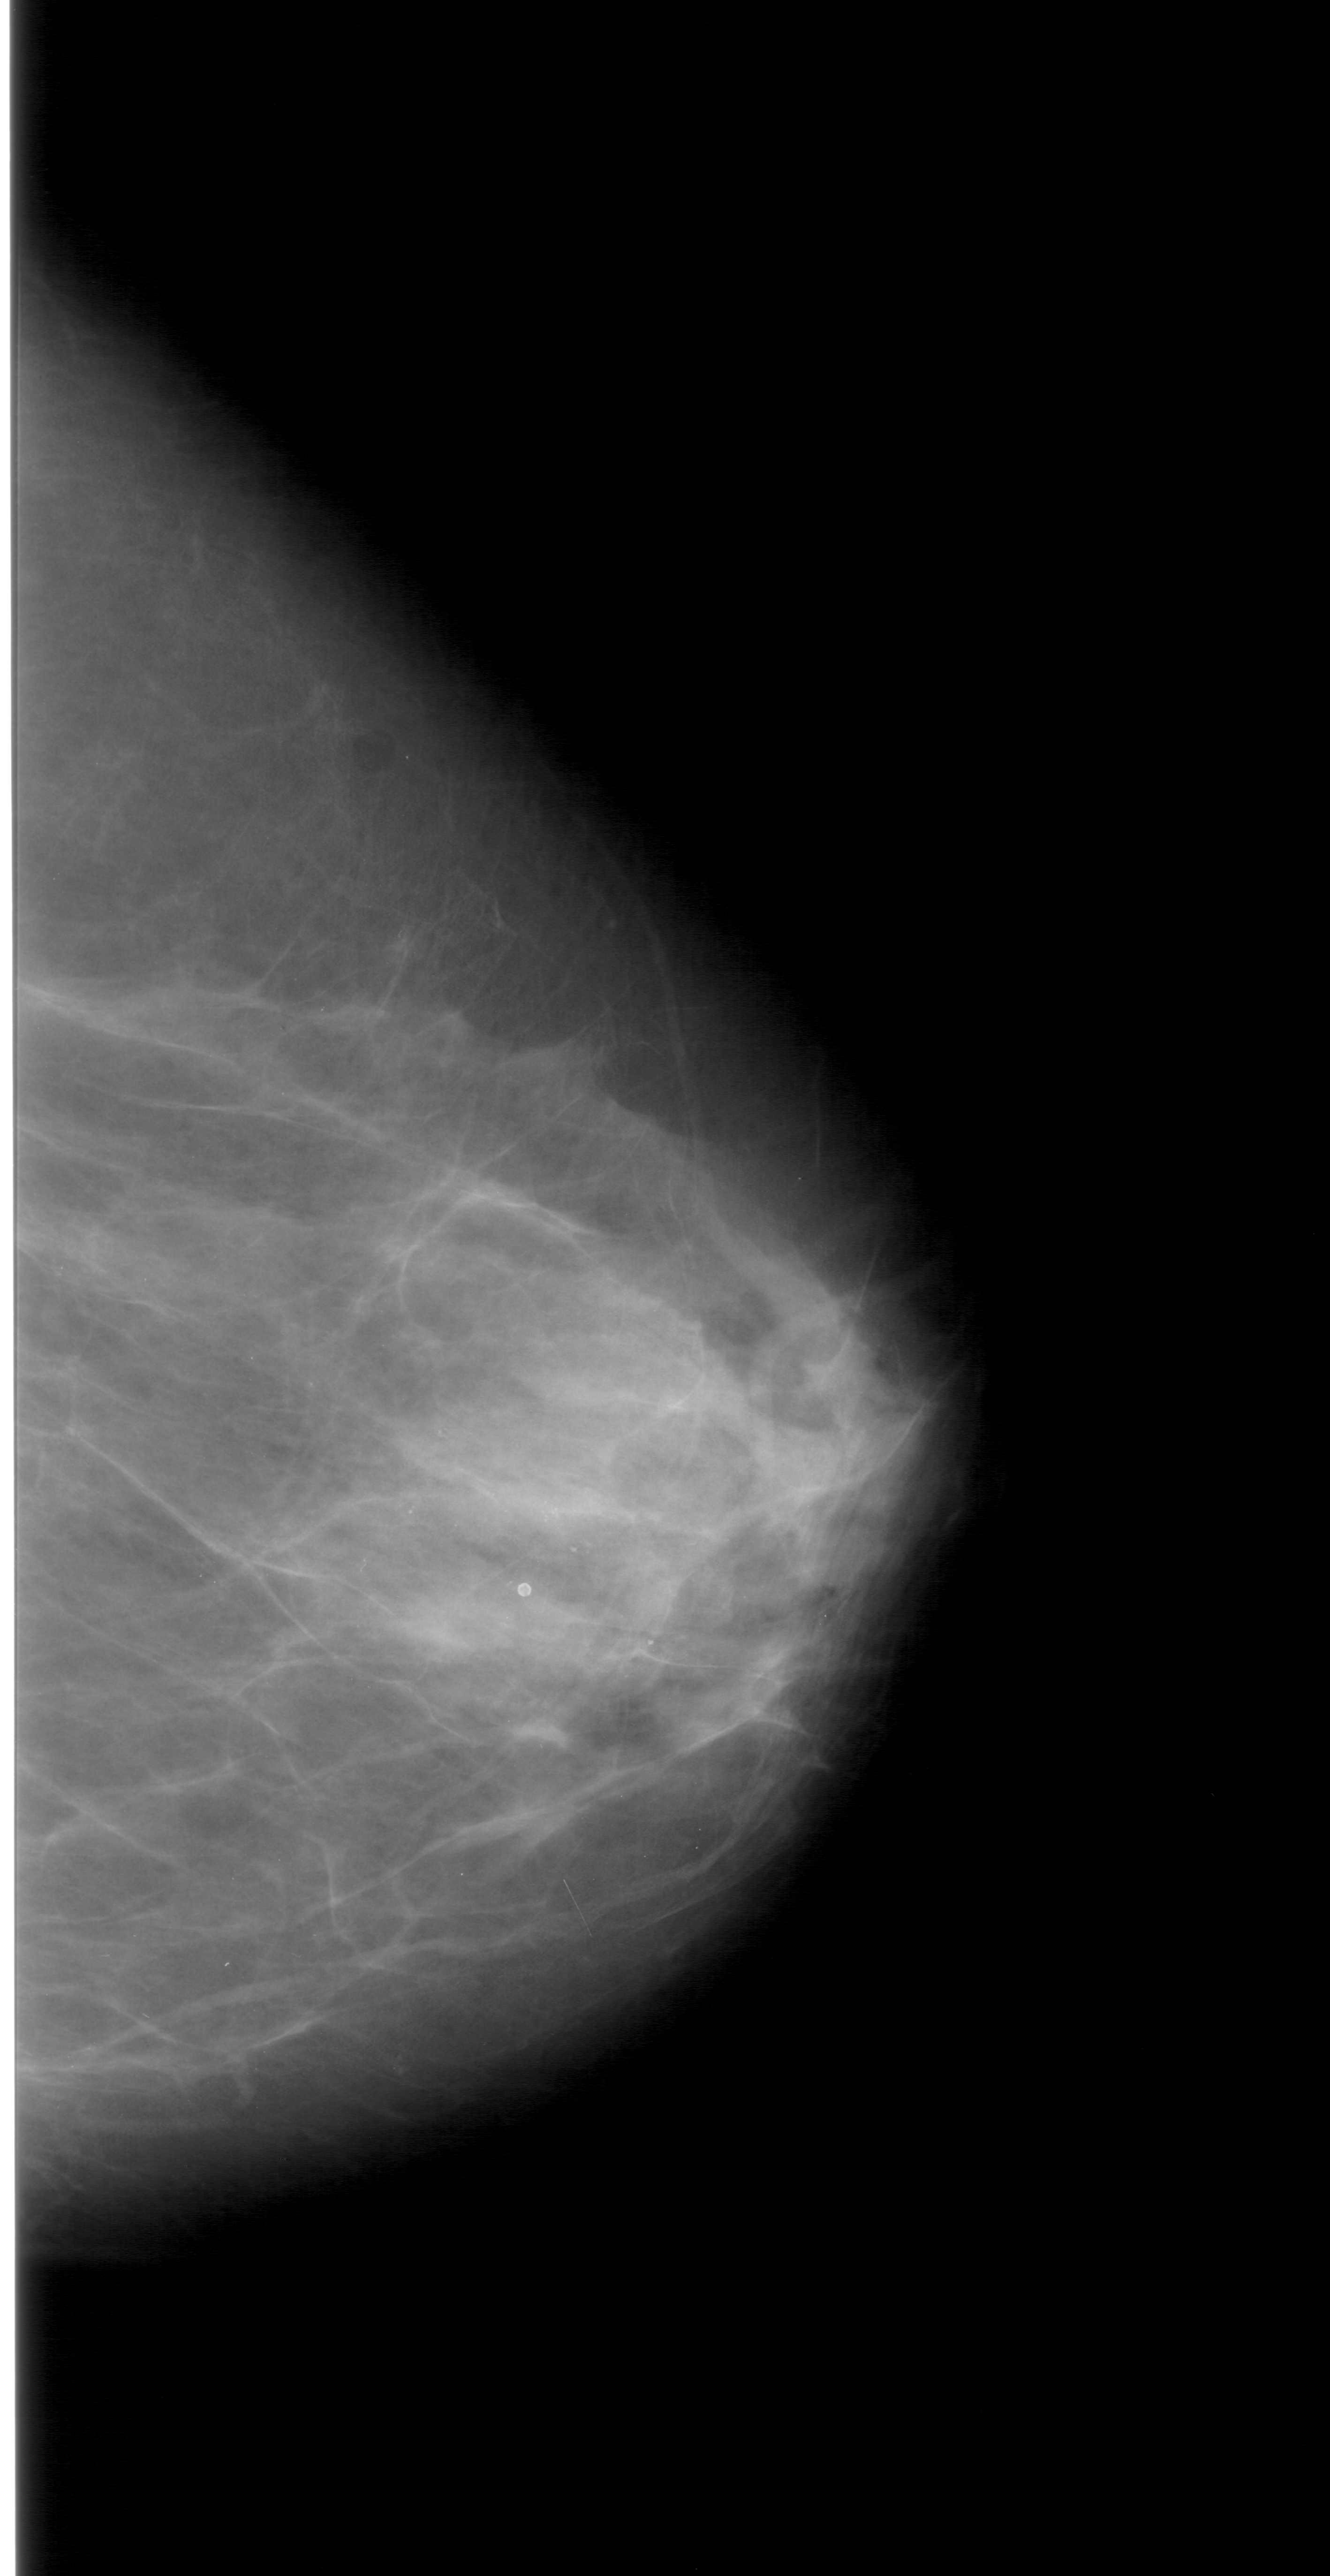
Digitized screen-film mammogram. Right breast. Craniocaudal (CC) view. Breast composition: extremely dense (BI-RADS density category 4 of 4). 1330 × 2576 image matrix.
Marked abnormalities (boxes around the expert regions of interest):
- calcifications, morphology pleomorphic, distribution linear; BI-RADS assessment category 4; pathology result (as recorded, not read from the image): benign: box from (x=294, y=1434) to (x=701, y=1765) px